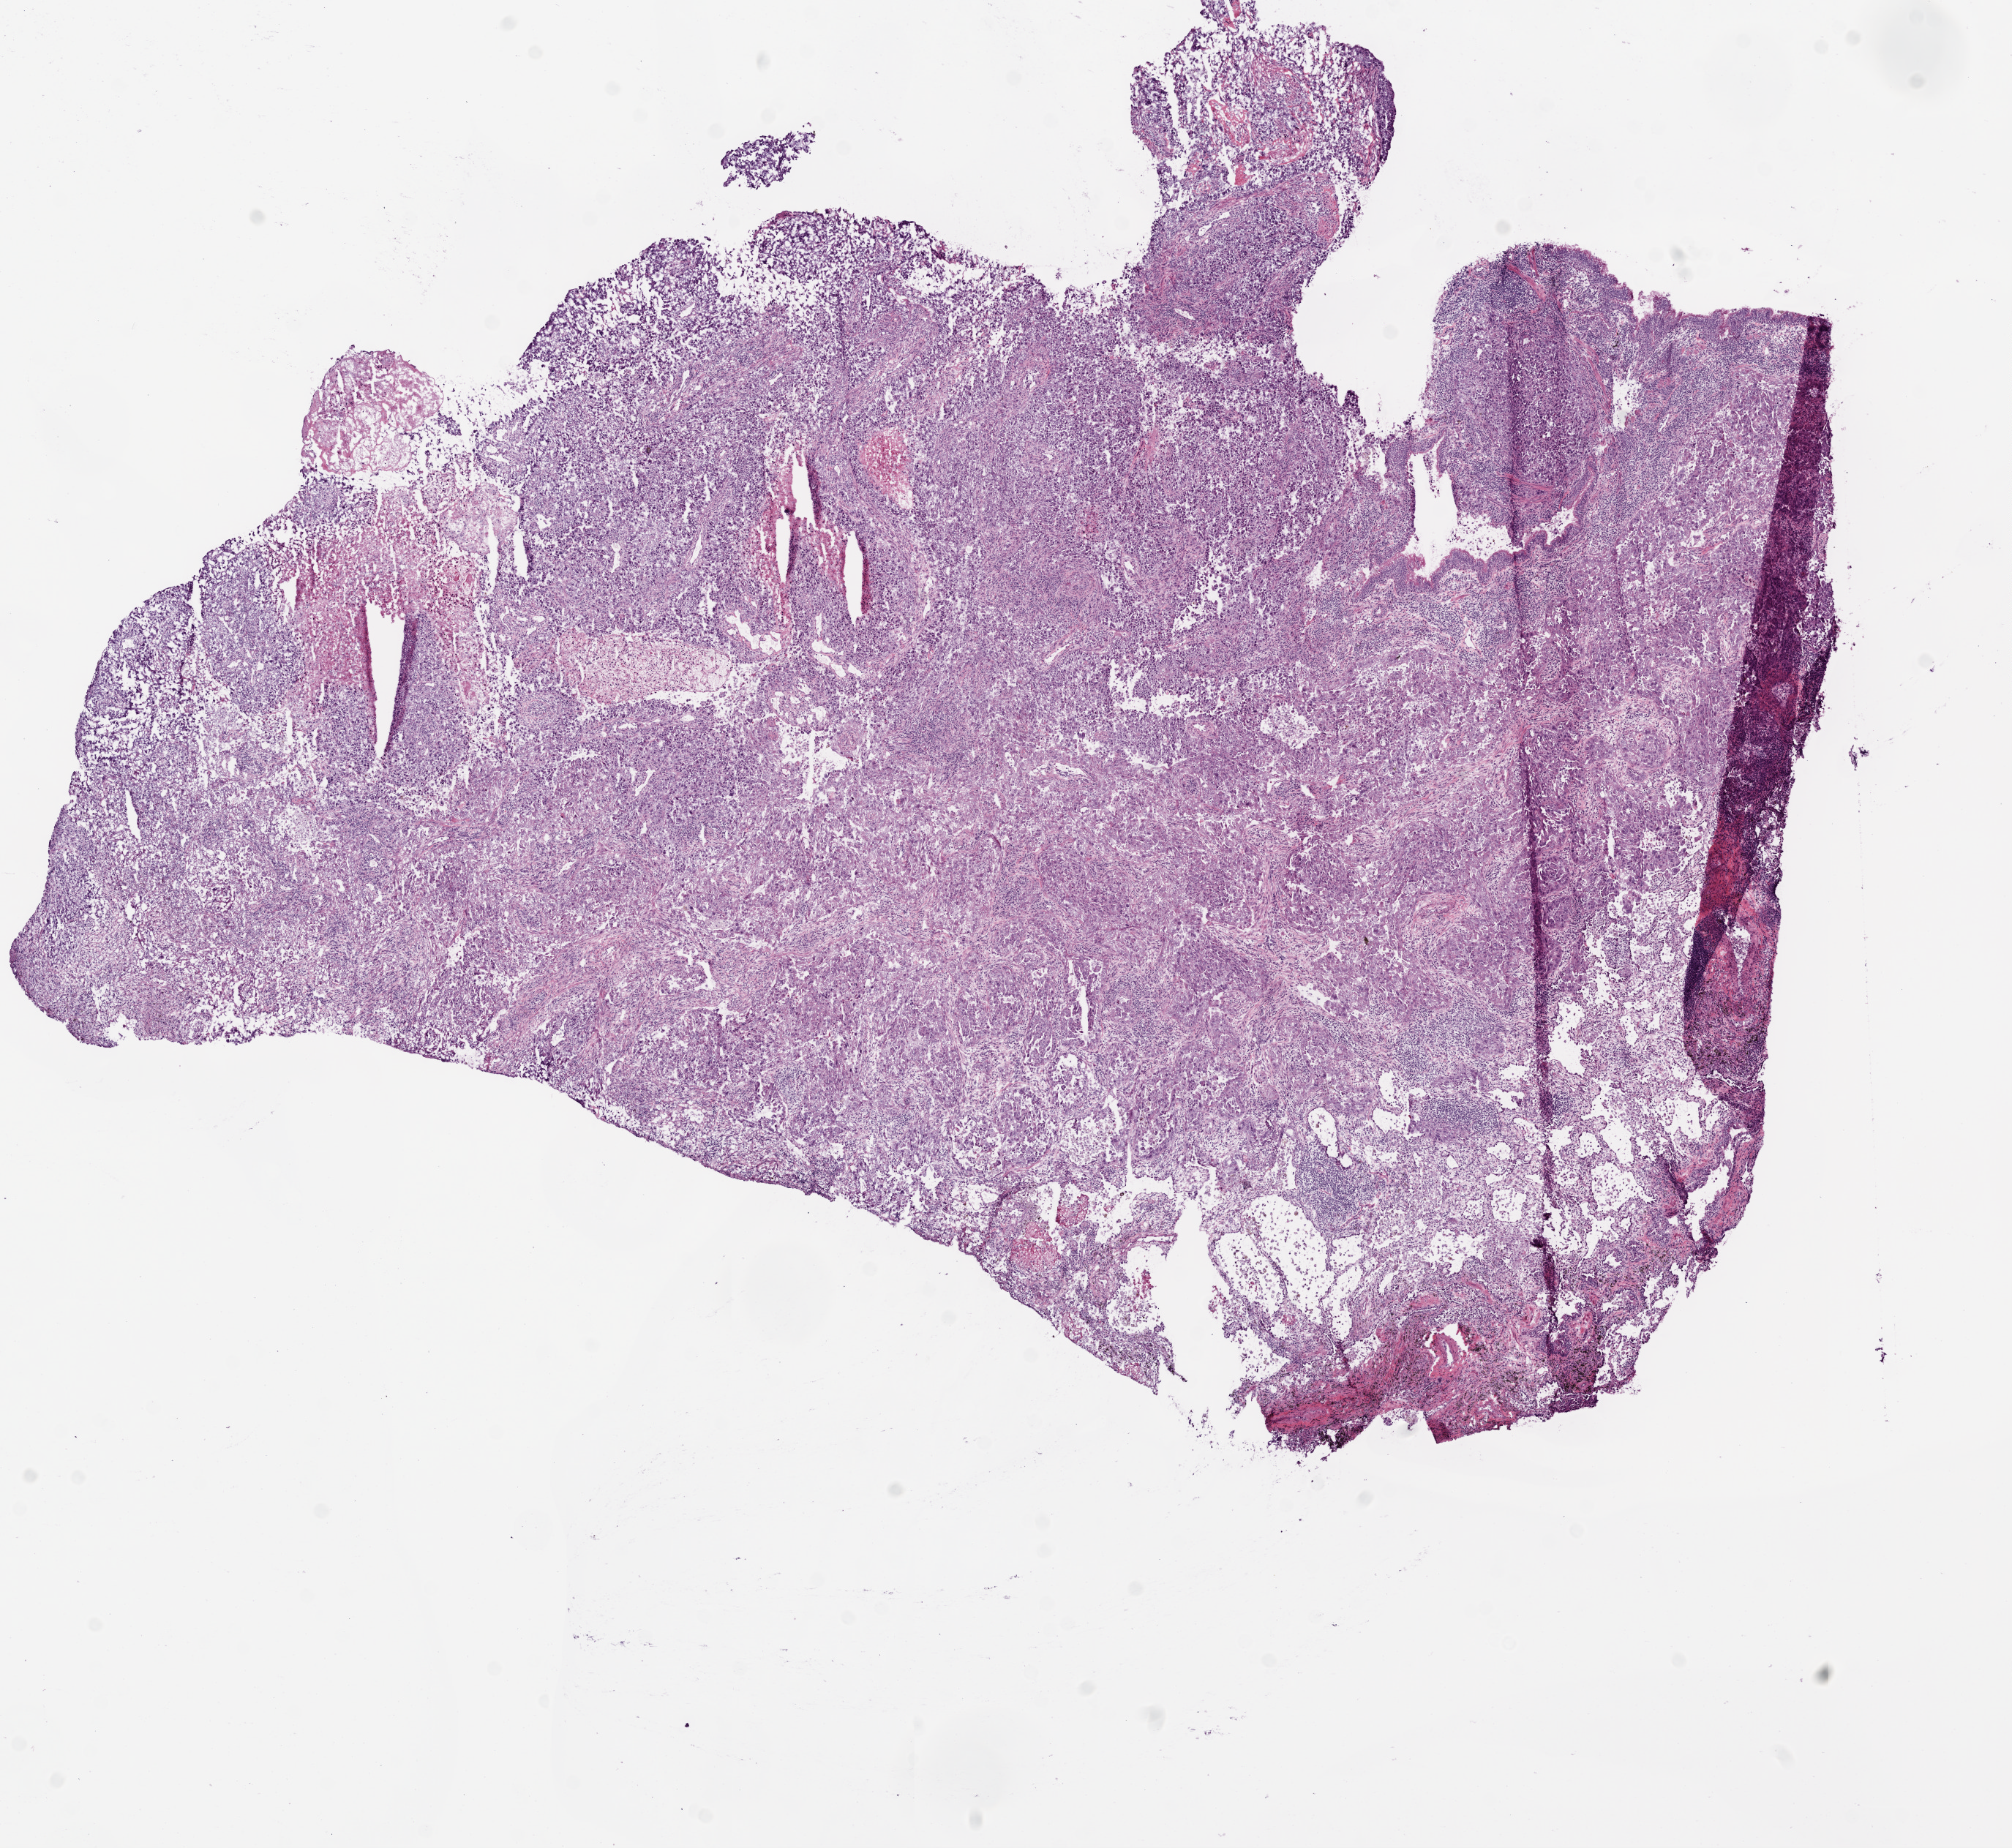
Whole-slide histology image, H&E, shown as a low-resolution overview of the whole scanned area (about 11.0 x 10.1 mm). Frozen section. Sample: primary tumour, lung. Male patient; age at initial diagnosis 42 years. Pathologist review of this section (percent, as recorded): tumour cells 75%, tumour nuclei 70%, normal cells 10%, stromal cells 5%, necrosis 10%.
* AJCC pathologic stage: IV (5th edition)
* histologic diagnosis: Adenocarcinoma, NOS (upper lobe, lung)
* TNM: T2 N1 M1